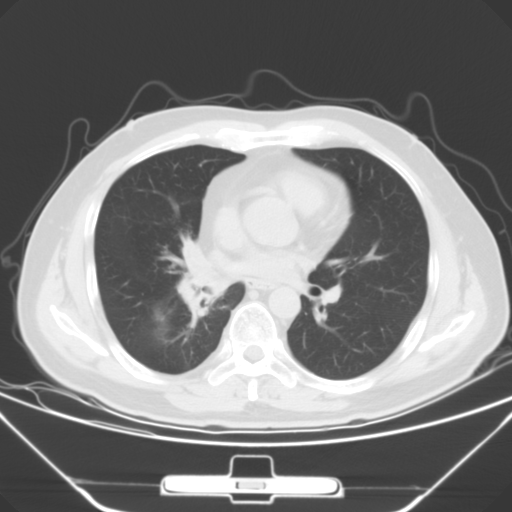
Chest CT, one axial slice; 120 kVp; lung window (W 1500 / L -600 HU); 512 × 512 image matrix, field of view 371 × 371 mm. Male patient, age 48 years. Case-level facts recorded for this patient, not image findings: clinical TNM (as recorded): T1a N1 M1c; histopathological grade: G3.
Annotated regions visible in this slice (rectangle marked by the reading radiologist):
- lung tumour (recorded histology: adenocarcinoma): bounding box [x1, y1, x2, y2] px = [169, 233, 222, 320]